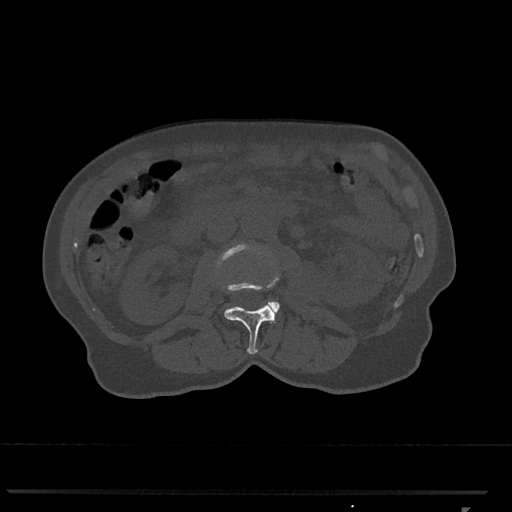
CT including the spine, one axial slice; position 317 of 793 along the scan axis; bone window (W 1800 / L 400 HU); 0.5 mm slice thickness; 512 × 512 image matrix. Female patient, age 62 years. From the clinical record (not read from this slice): primary cancer: renal.
Annotated regions visible in this slice (semi-automatically segmented with operator editing):
- L2 vertebra: box from (x=217, y=243) to (x=279, y=354) px
- L3 vertebra: (x=268, y=301)–(x=280, y=311)